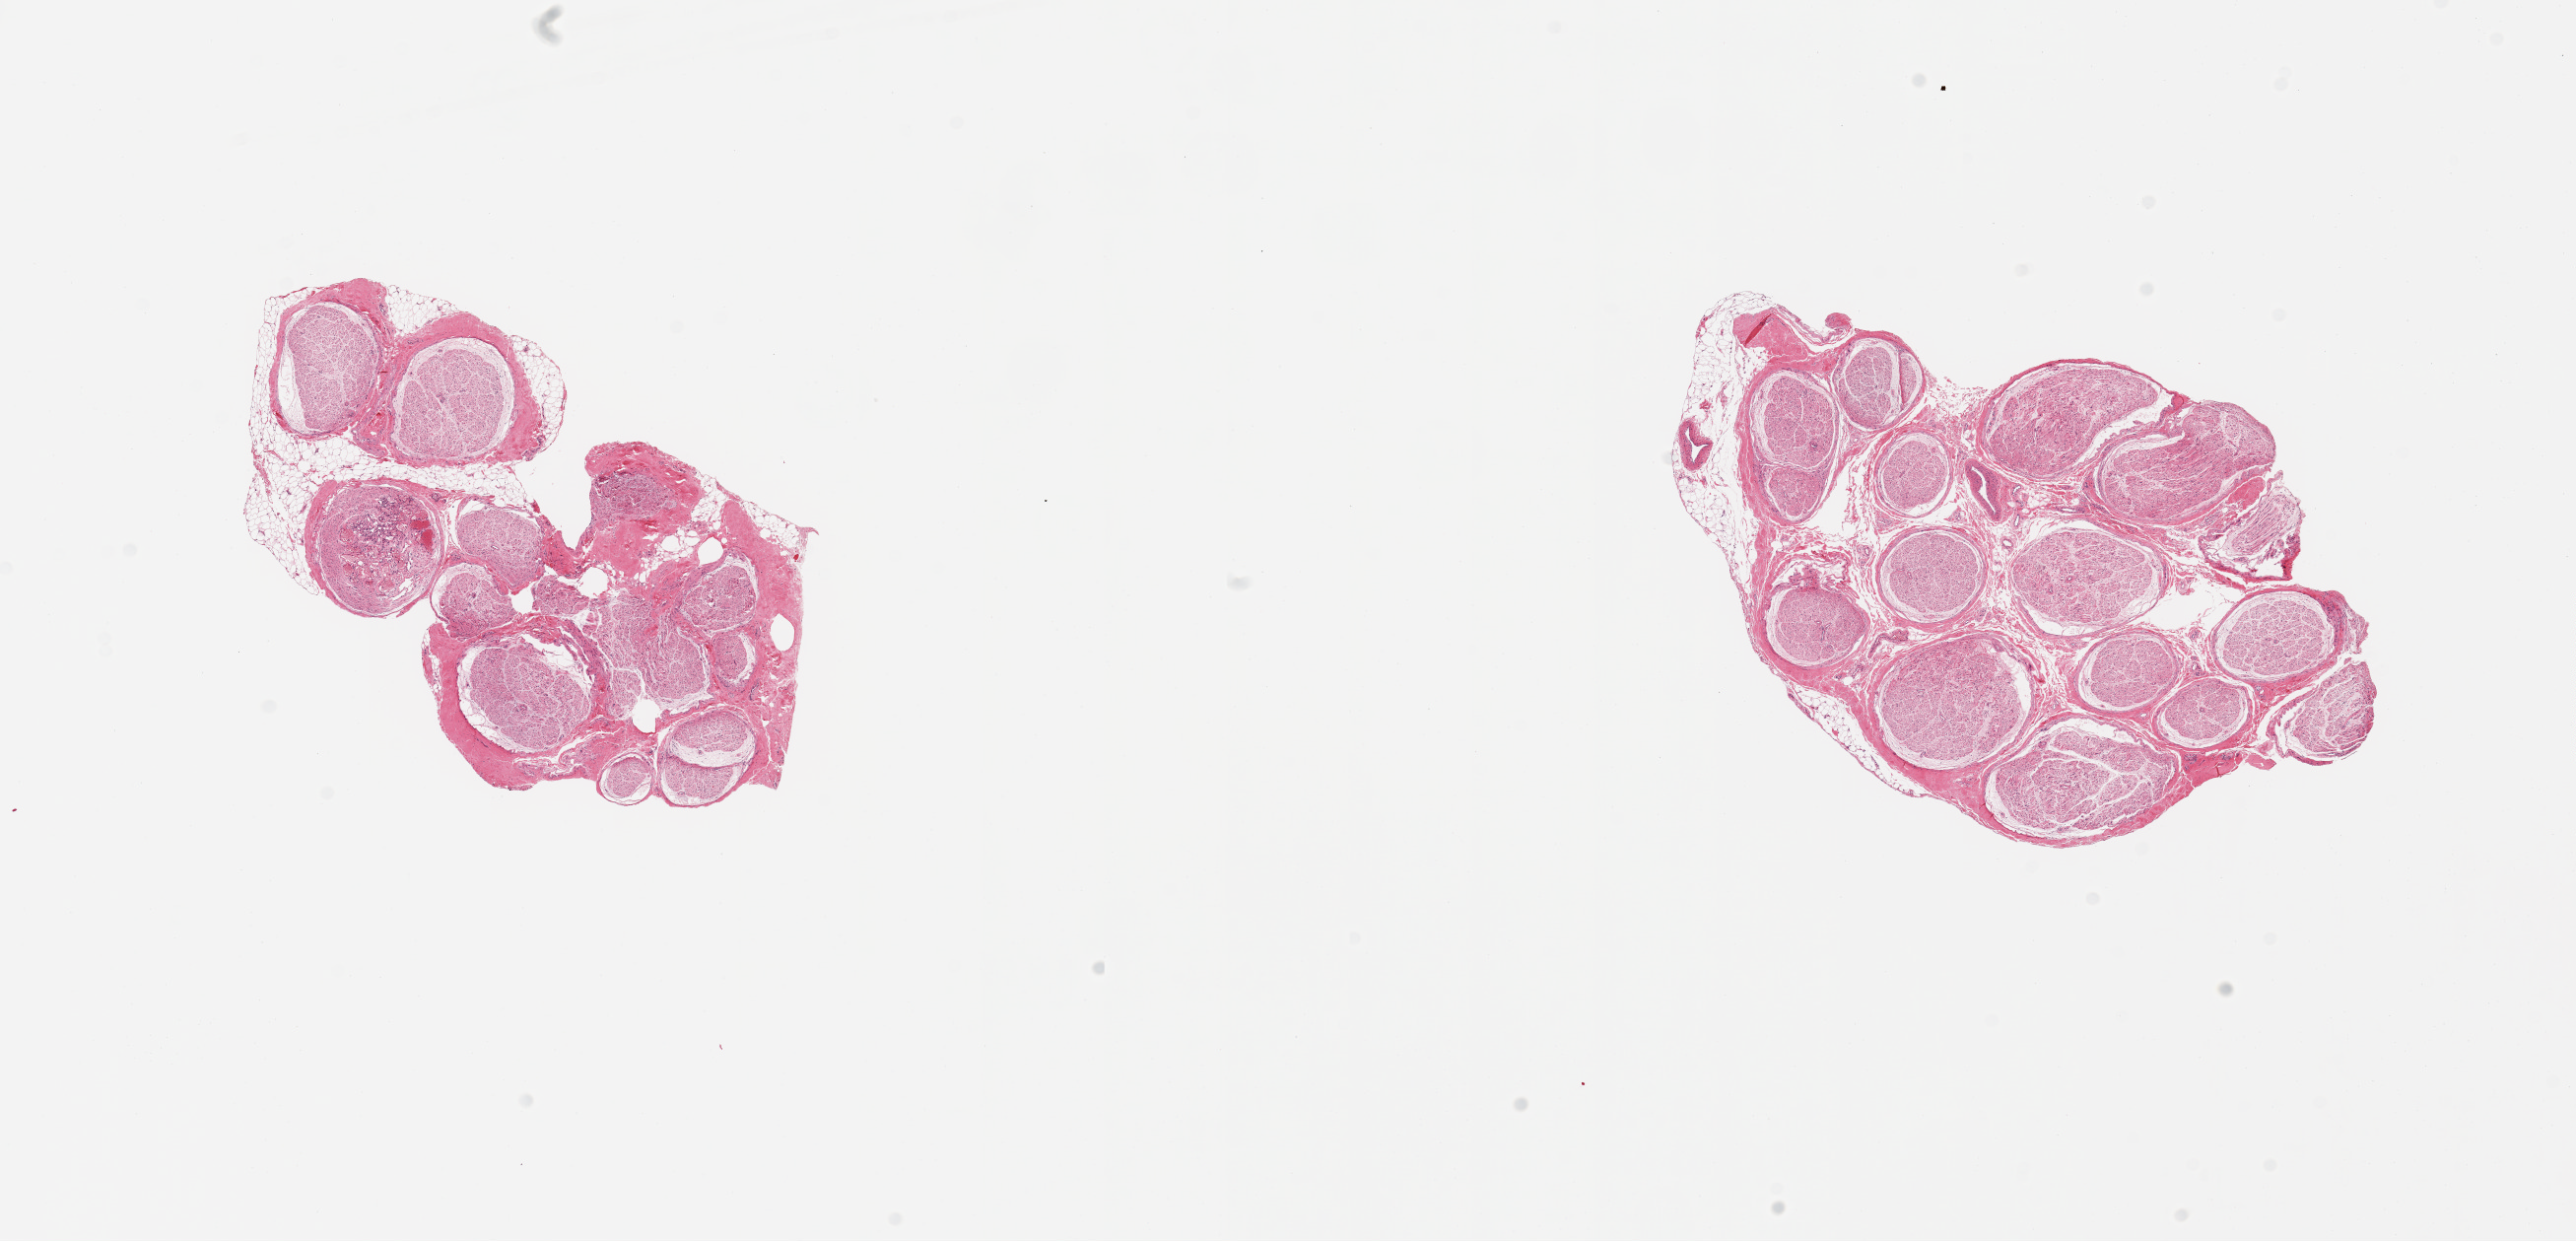
Haematoxylin and eosin whole-slide image, brightfield — shown as a low-resolution overview of the whole scanned area (about 20.7 x 10.0 mm, acquisition: 20x scan), PAXgene-fixed paraffin-embedded (PFPE) section, target tissue: tibial nerve, donor tissue sample. Donor: male.
- pathologist's review note for this sample: 2 pieces, good specimens, trace nubbin adherent fat, 0.5mm thick